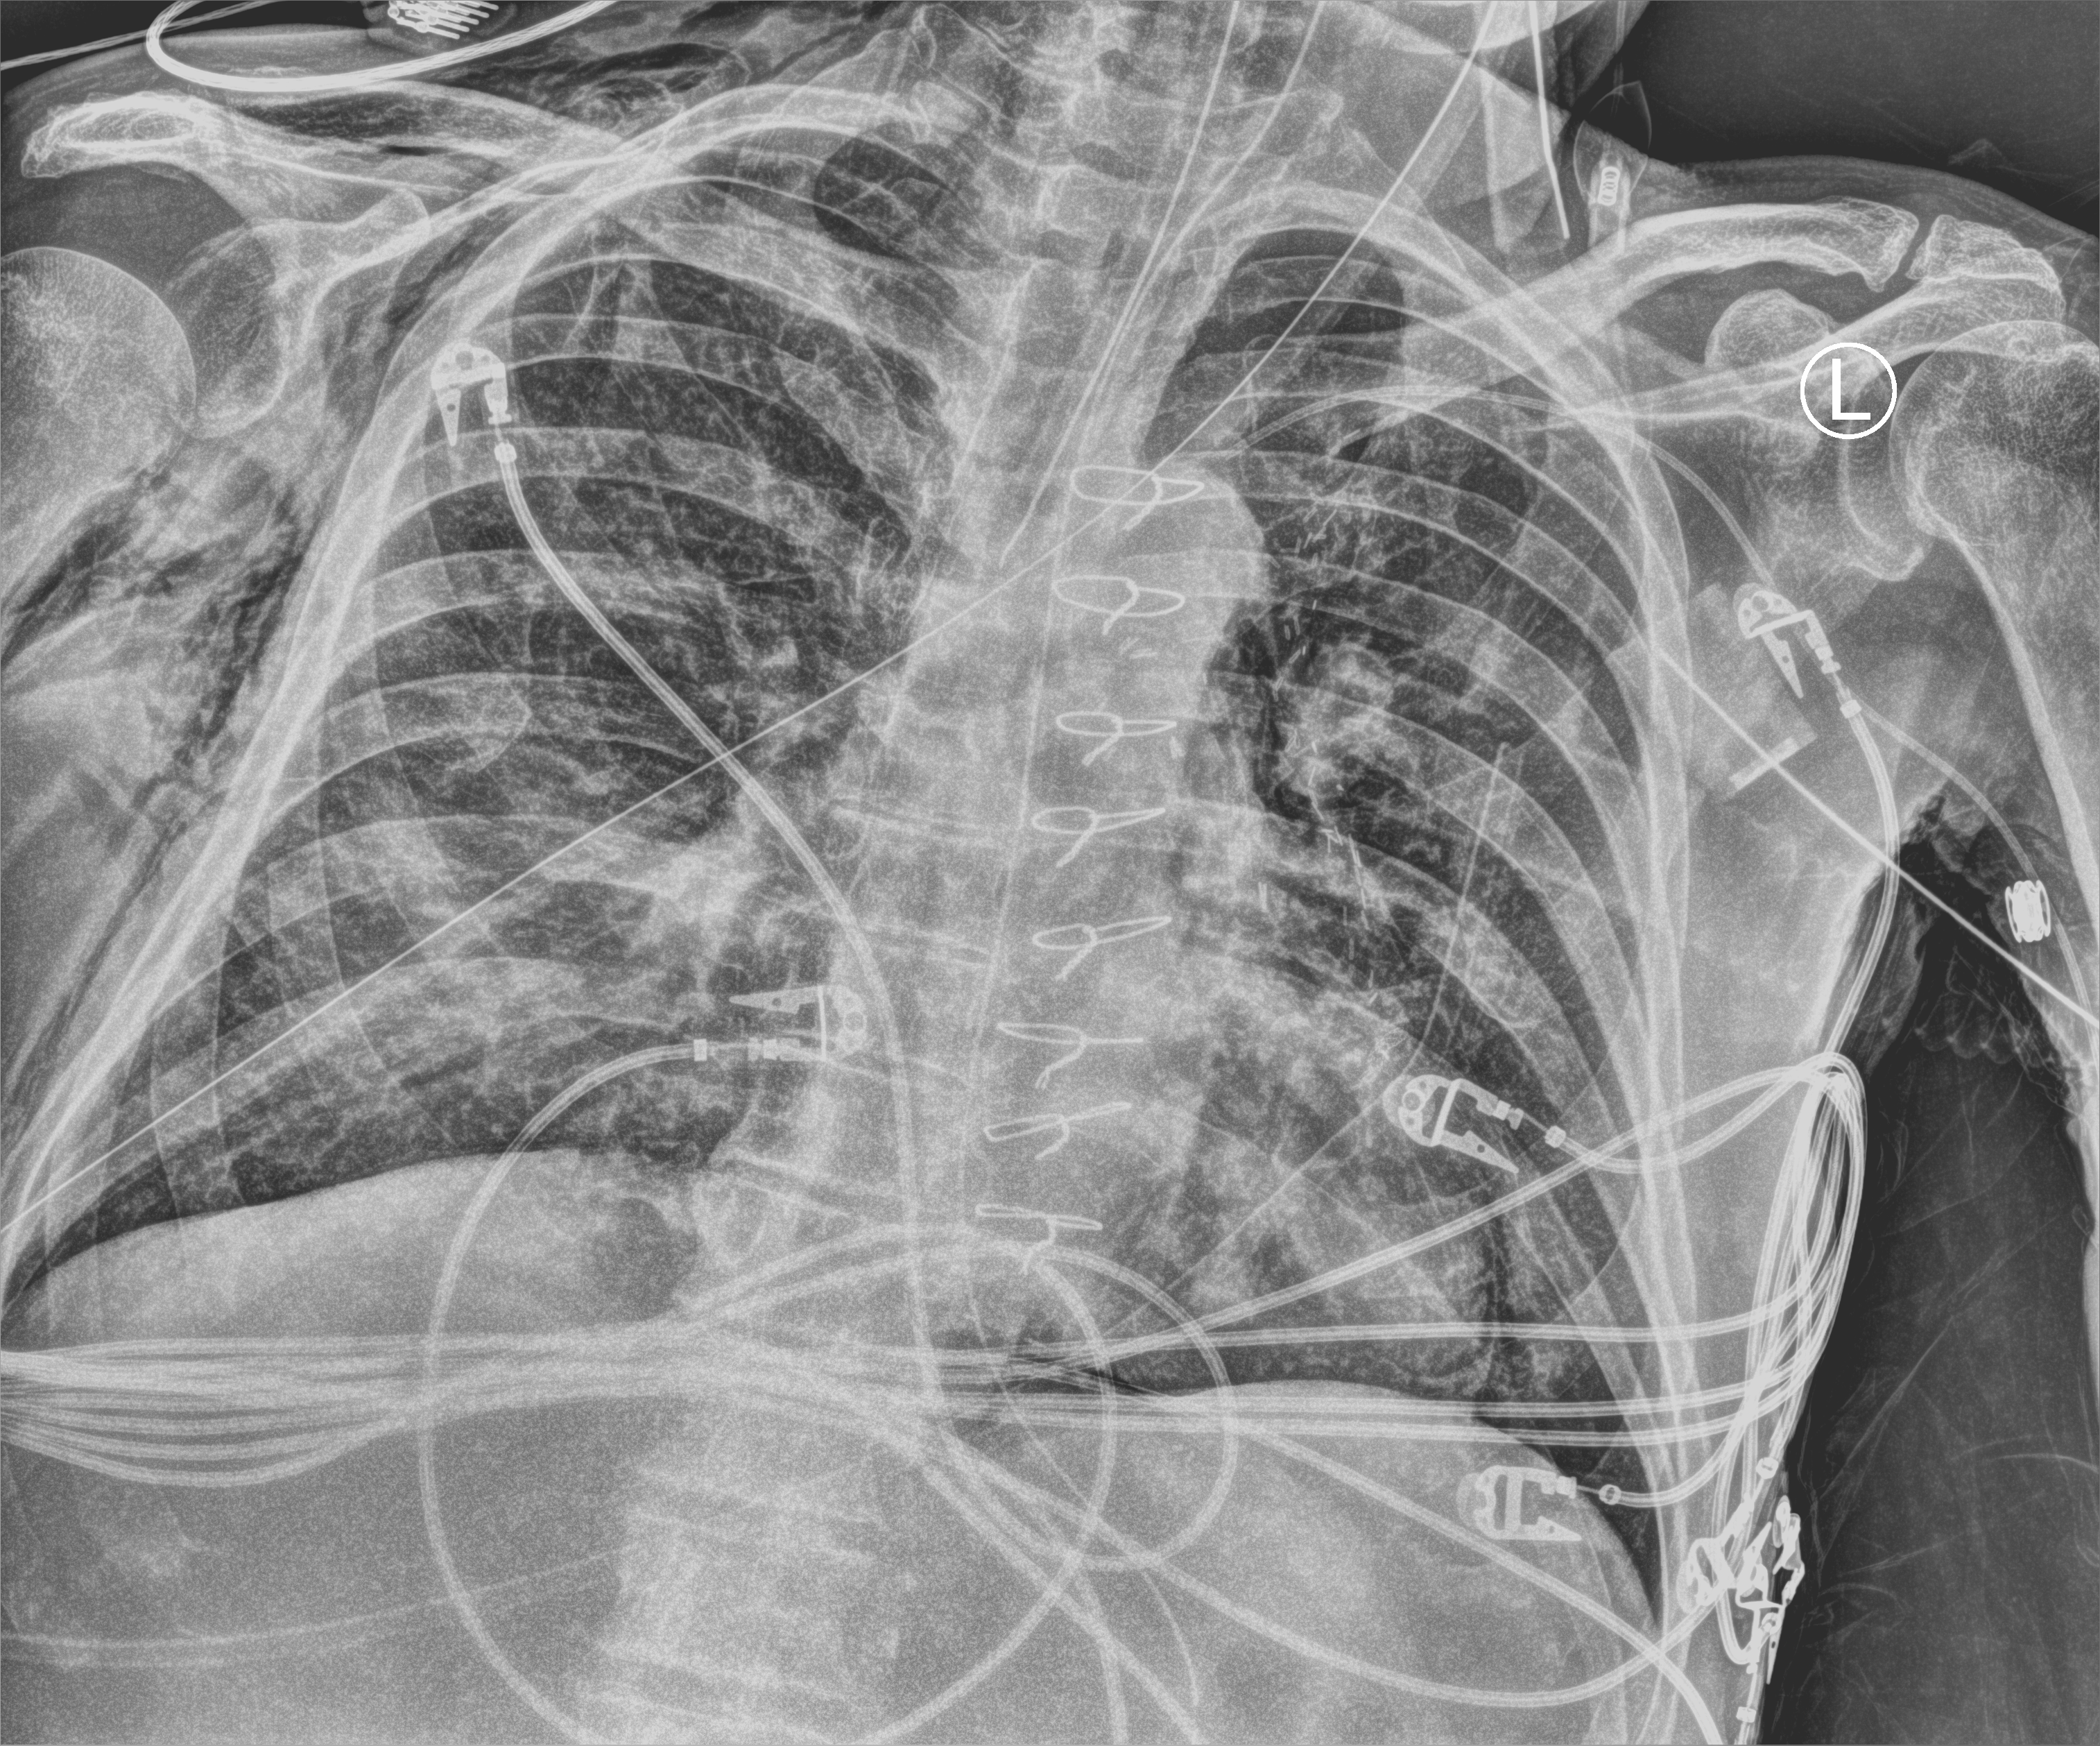
Portable chest radiograph, anteroposterior (AP) projection. Male patient hospitalised with COVID-19, age 60–74 years.
From the hospital-stay record, not from the radiograph (when in the stay this image was taken is not recorded):
- mechanically ventilated during this hospital stay: yes
- COPD (admission record): no
- length of hospital stay: 22 days